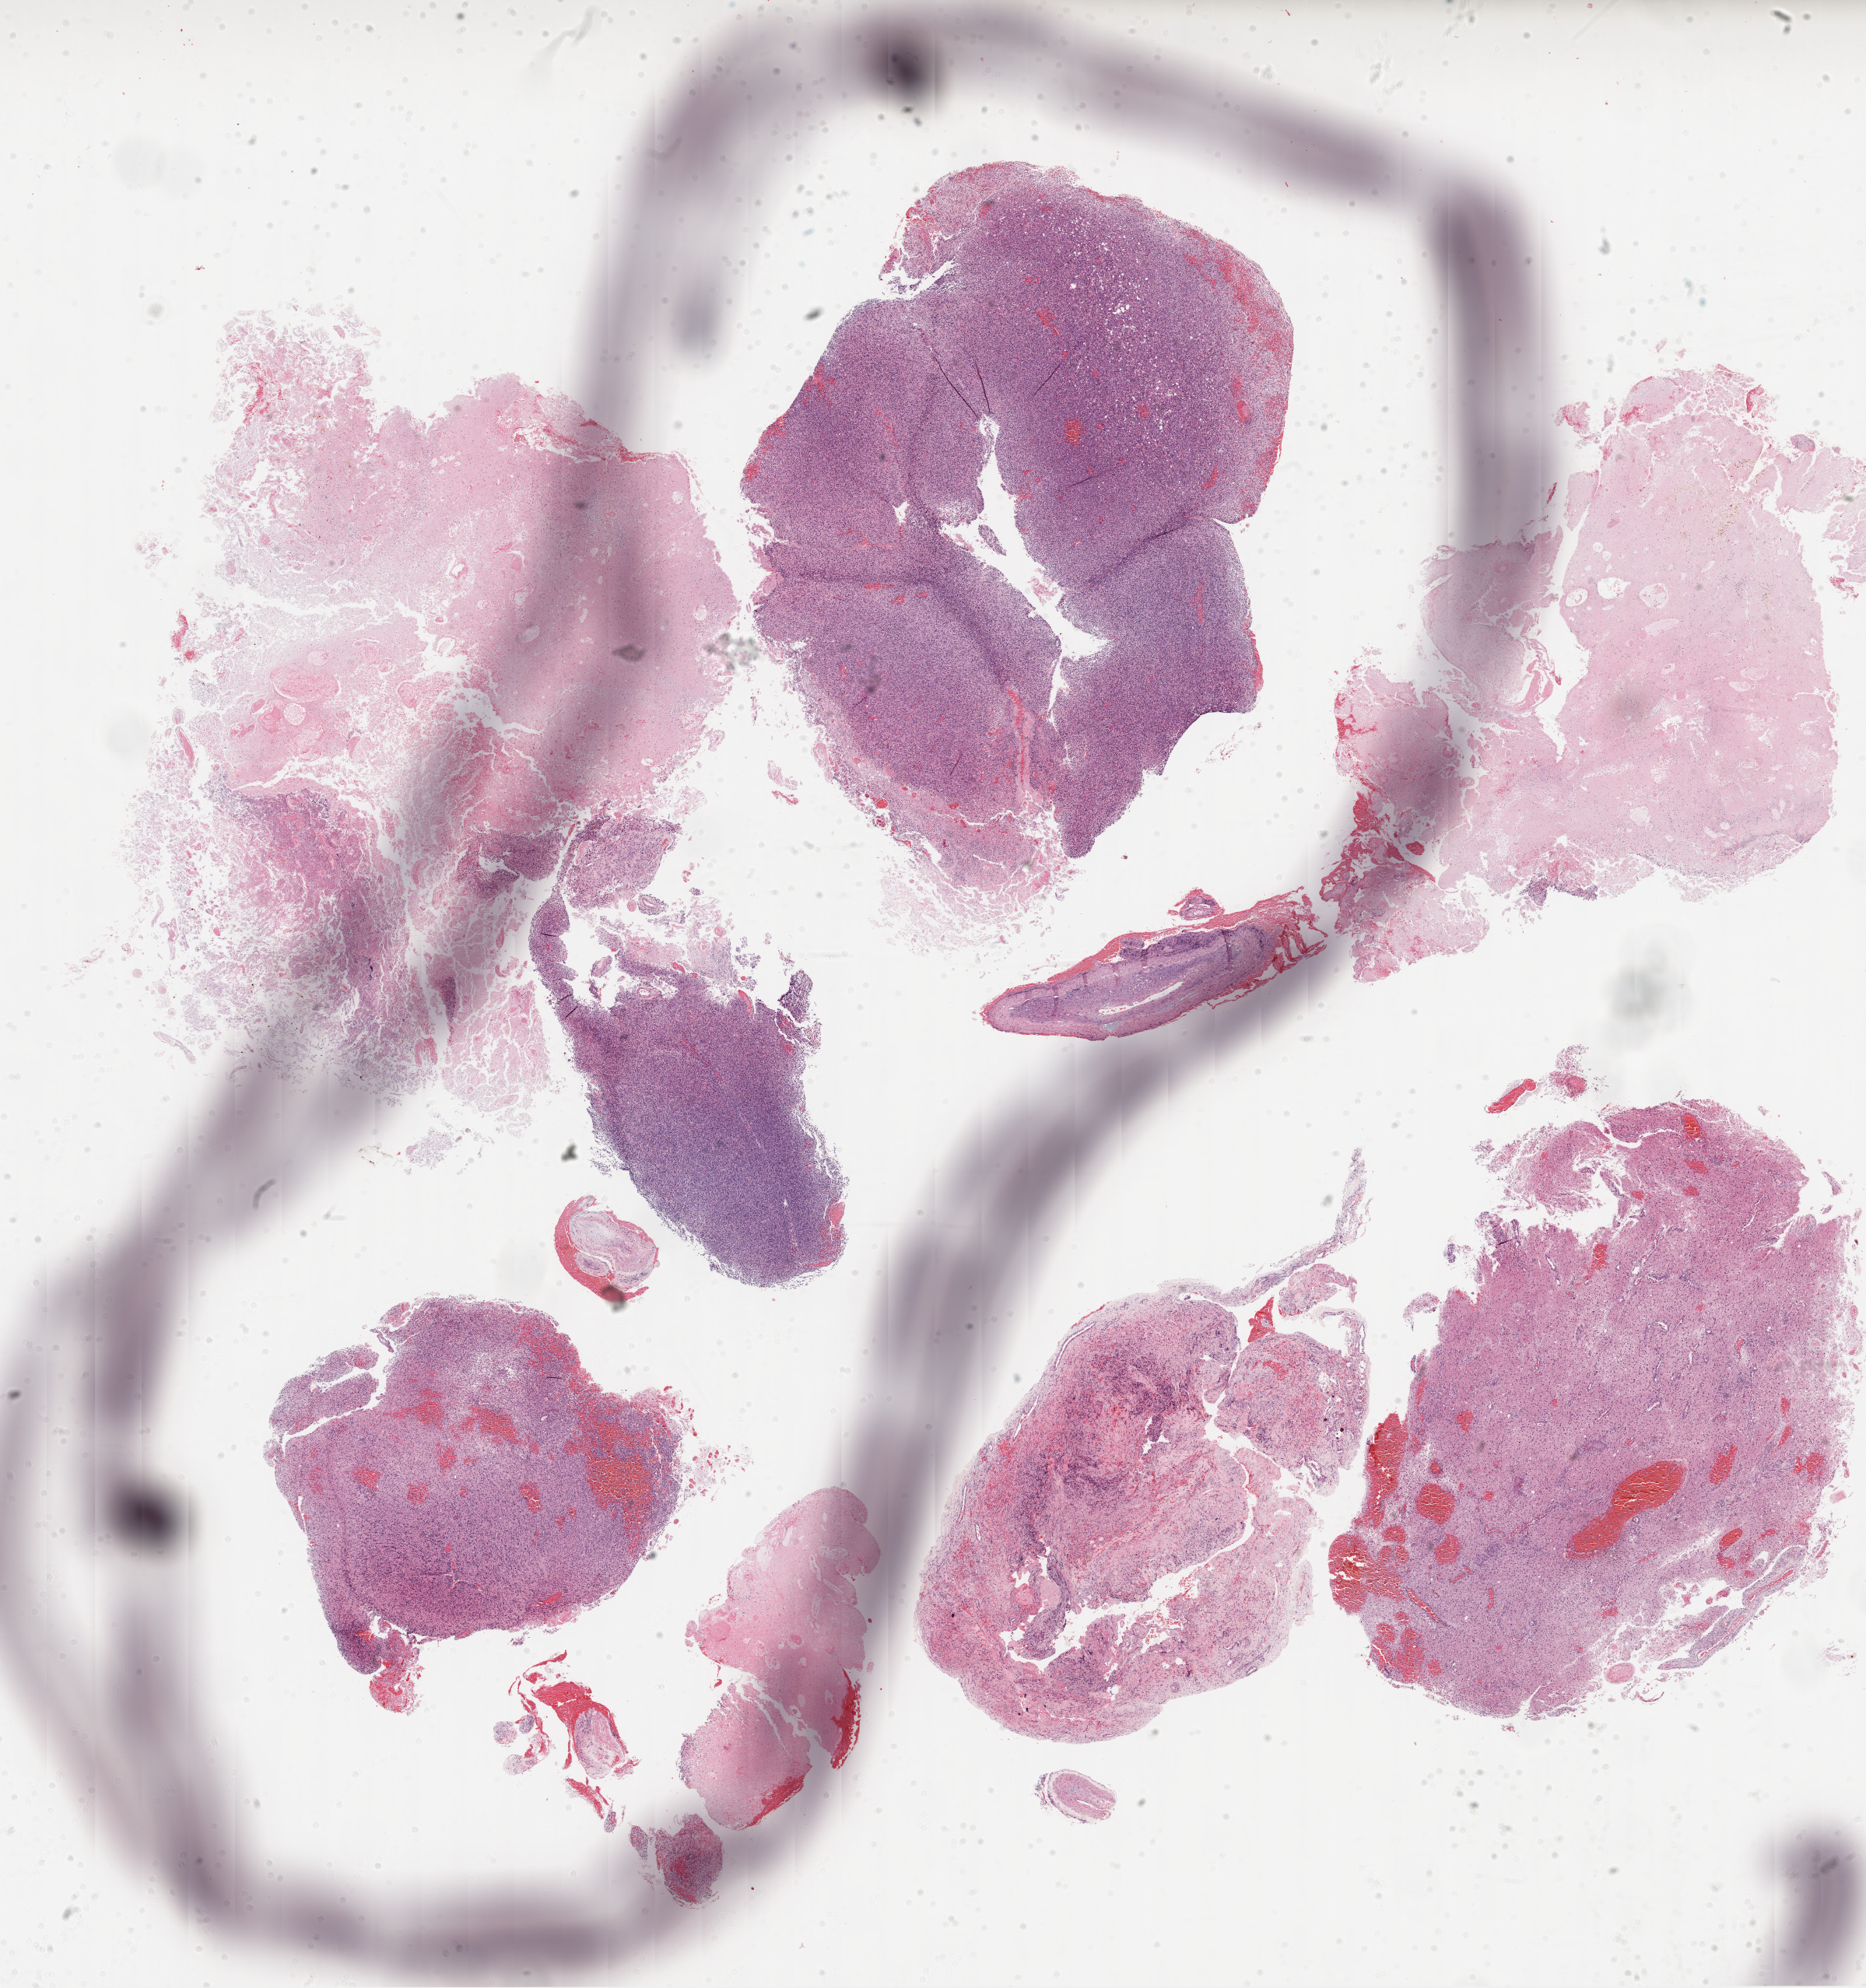
Digitized H&E tissue section (whole slide), whole scanned area (about 19.3 x 20.6 mm, from a 20x scan) shown as a low-resolution overview, FFPE section, sample: primary tumour, brain. Patient: male, age at initial diagnosis 69 years.
Pathologic diagnosis: Glioblastoma.